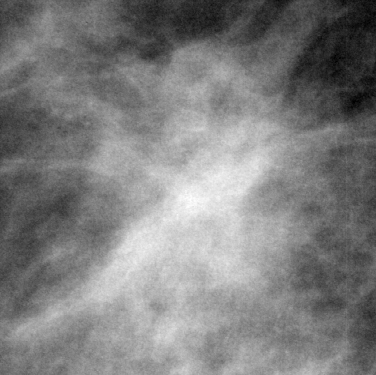
Crop from a digitized film mammogram around one marked abnormality; right breast; MLO view.
Marked abnormality: mass, shape irregular, margins ill defined; BI-RADS assessment category 4; pathology result (as recorded, not read from the image): malignant.